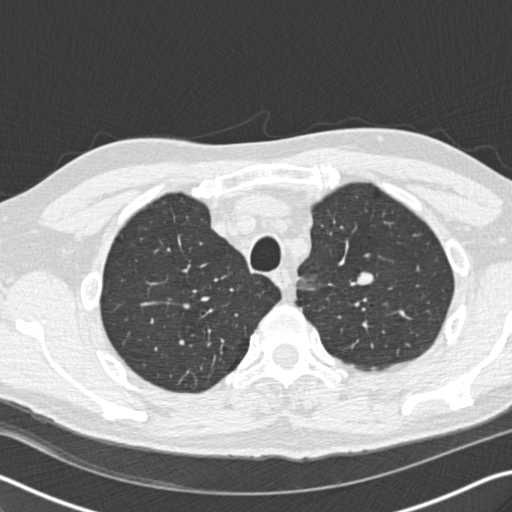
Chest CT (low-dose screening protocol), one axial image. Baseline annual screen. Lung window (W 1500 / L -600 HU). Standard (soft-tissue) reconstruction kernel (B30f). Slice 40 of 208 in the series. 512 × 512 image matrix. Male participant, aged 56 years at enrolment. Current smoker at enrolment.
Expert-annotated lung lesion, bounding box <340,261,388,300> (left, top, right, bottom; pixels). Reader record for this screening exam (exam-level; its link to the box is not recorded): non-calcified nodule or mass ≥4 mm, left upper lobe, 12 × 10 mm, smooth margins, soft tissue attenuation. Lung cancer was diagnosed 814 days after this screen (after the third annual screen): neuroendocrine carcinoma, NOS, left upper lobe, well differentiated (G1), stage IA (AJCC 6th edition), 20 mm at pathology.